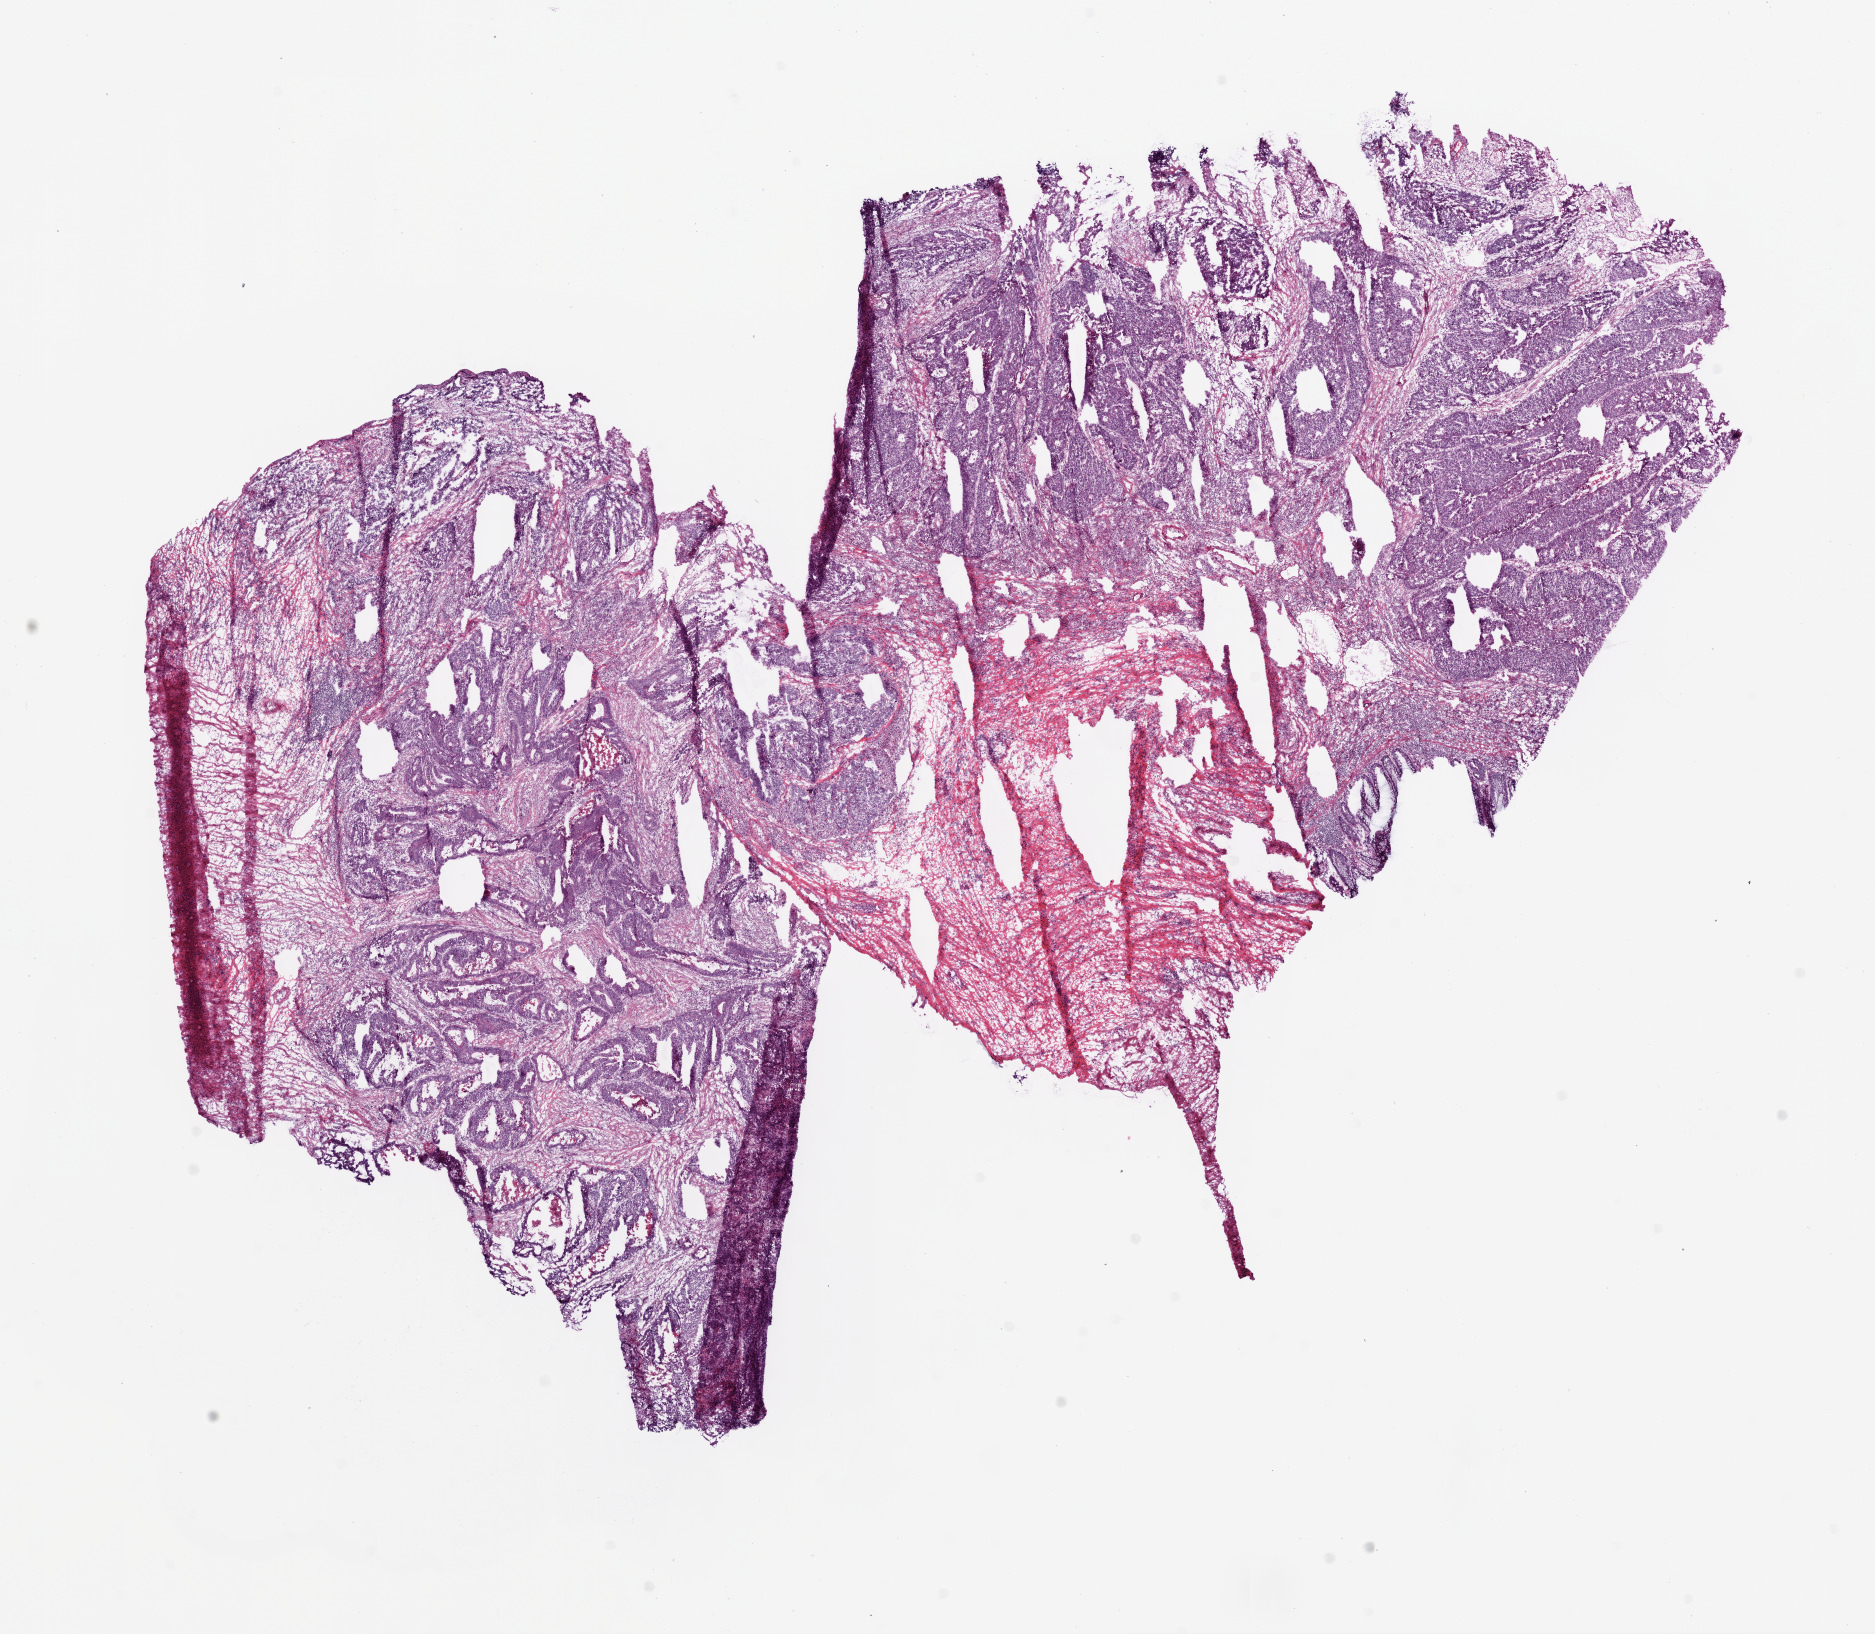
Digitized Hematoxylin and eosin (H&E) stained tissue section (whole slide) — whole scanned area (about 15.0 x 13.1 mm, acquisition: 20x scan) shown as a low-resolution overview. Frozen section. Sample: primary tumour, rectum. Male patient; age at initial diagnosis 65 years. Slide review estimates, as recorded: tumour cells 65%, tumour nuclei 65%, normal cells 15%, stromal cells 15%, necrosis 5%.
Histologic diagnosis: Adenocarcinoma, NOS. Lymph nodes positive (case pathology): 3 of 34 examined. AJCC pathologic stage: IV (5th edition).